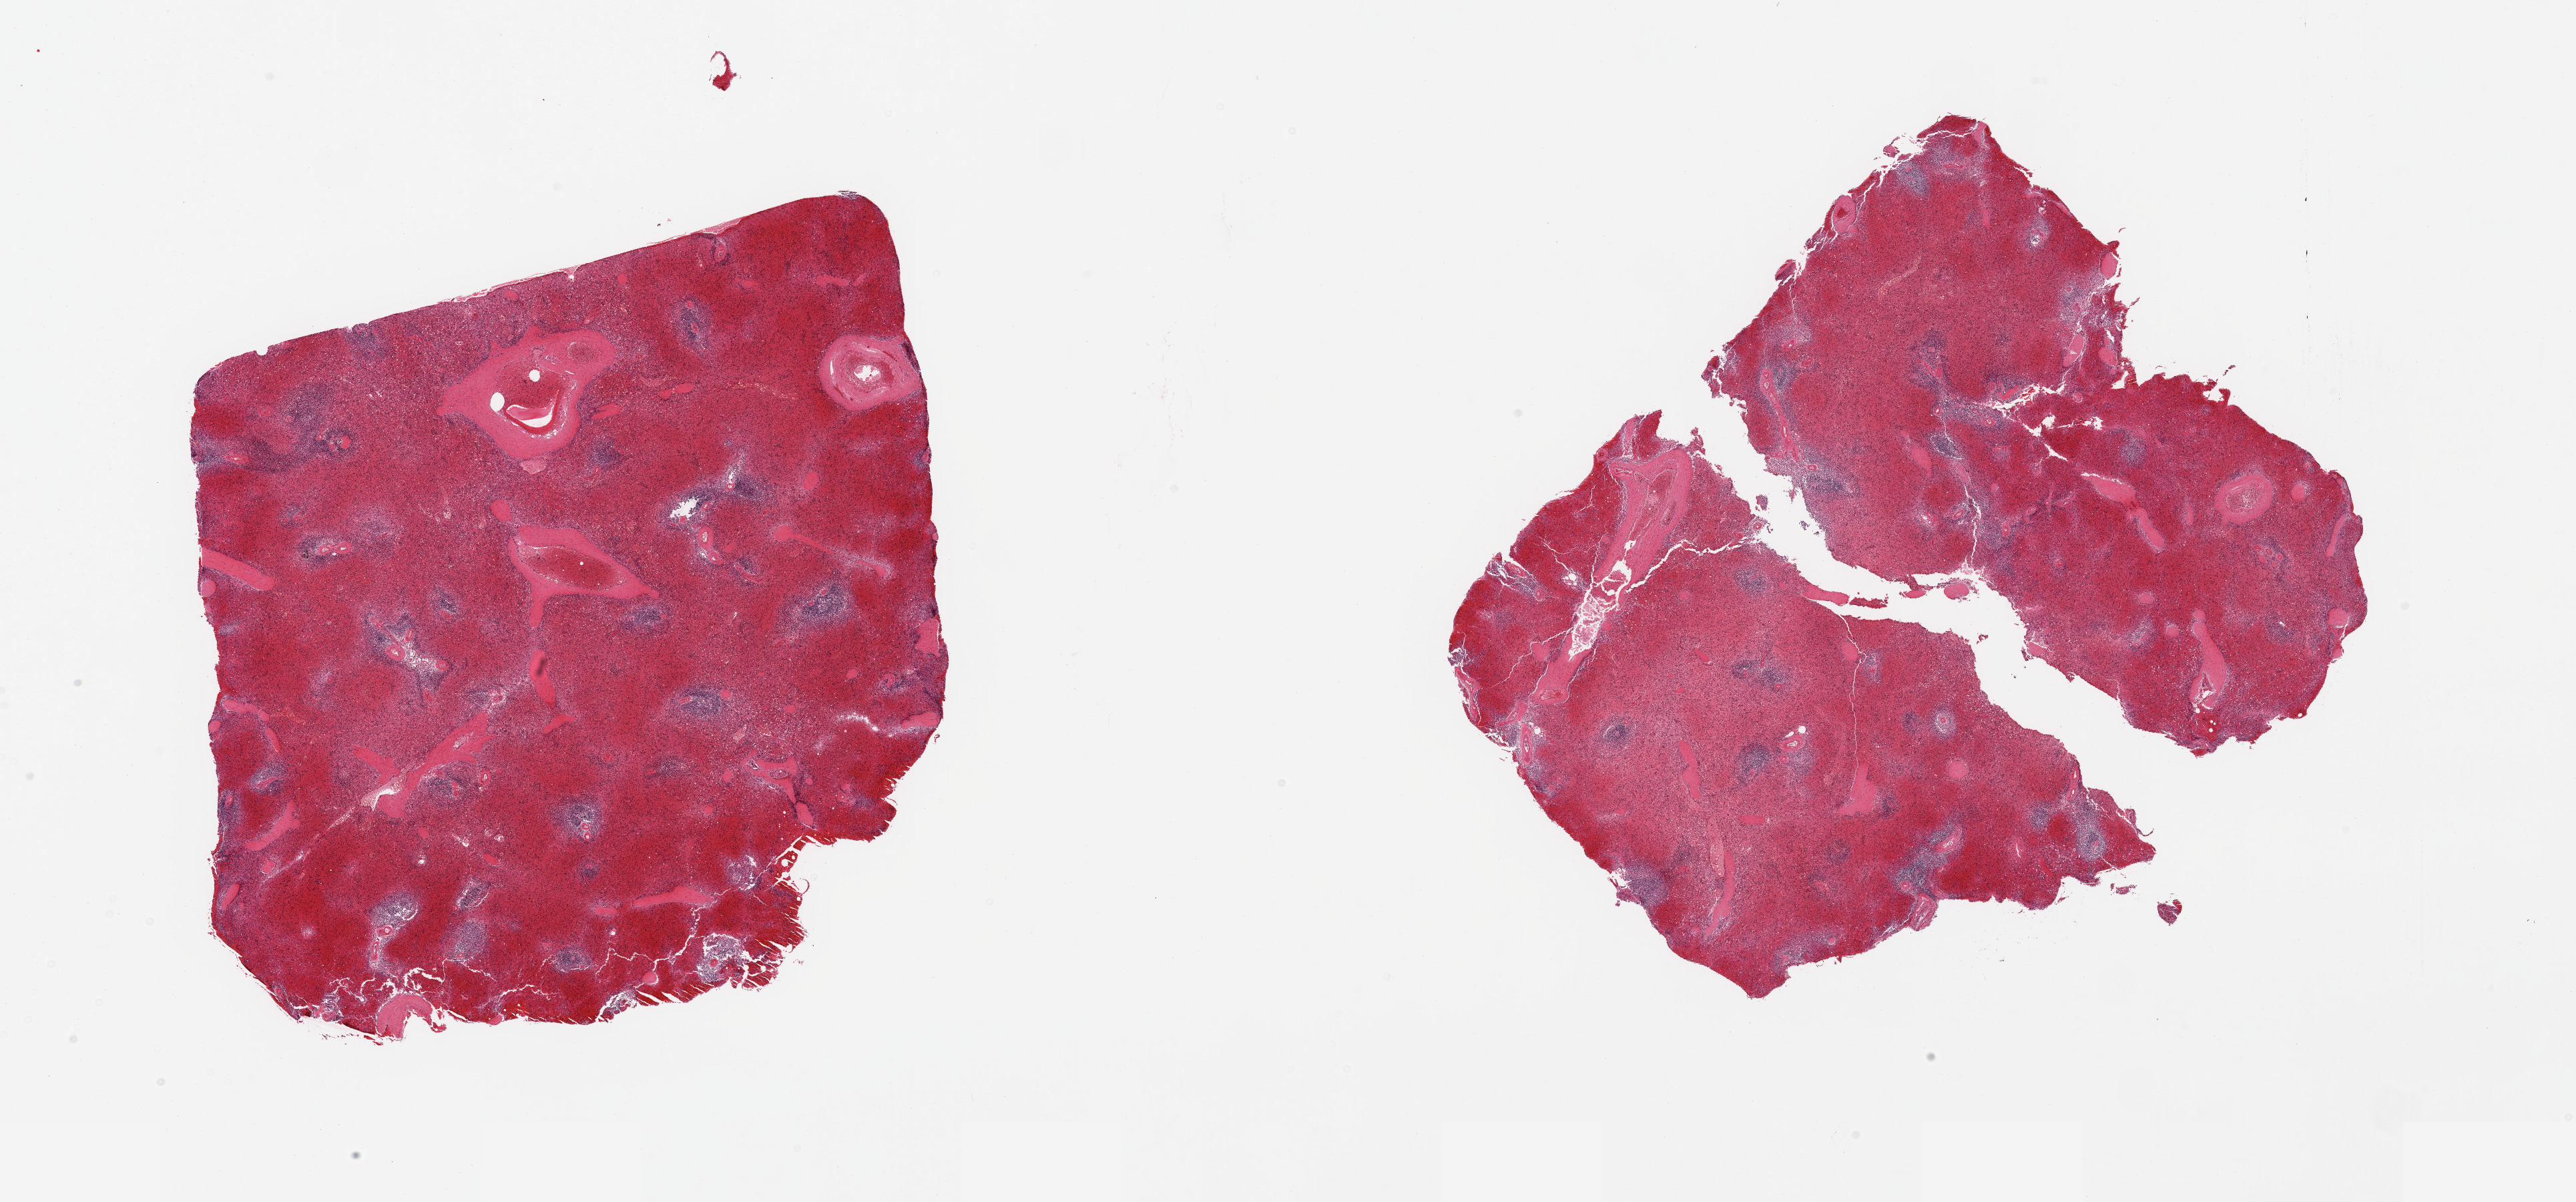
Digitized H&E-stained section, low-resolution overview of the scanned area, about 30.5 x 14.2 mm, PAXgene-fixed paraffin-embedded (PFPE) section, target tissue: spleen, tissue donor sample. Donor: male.
- review note (as recorded): 2 pieces; severely congested